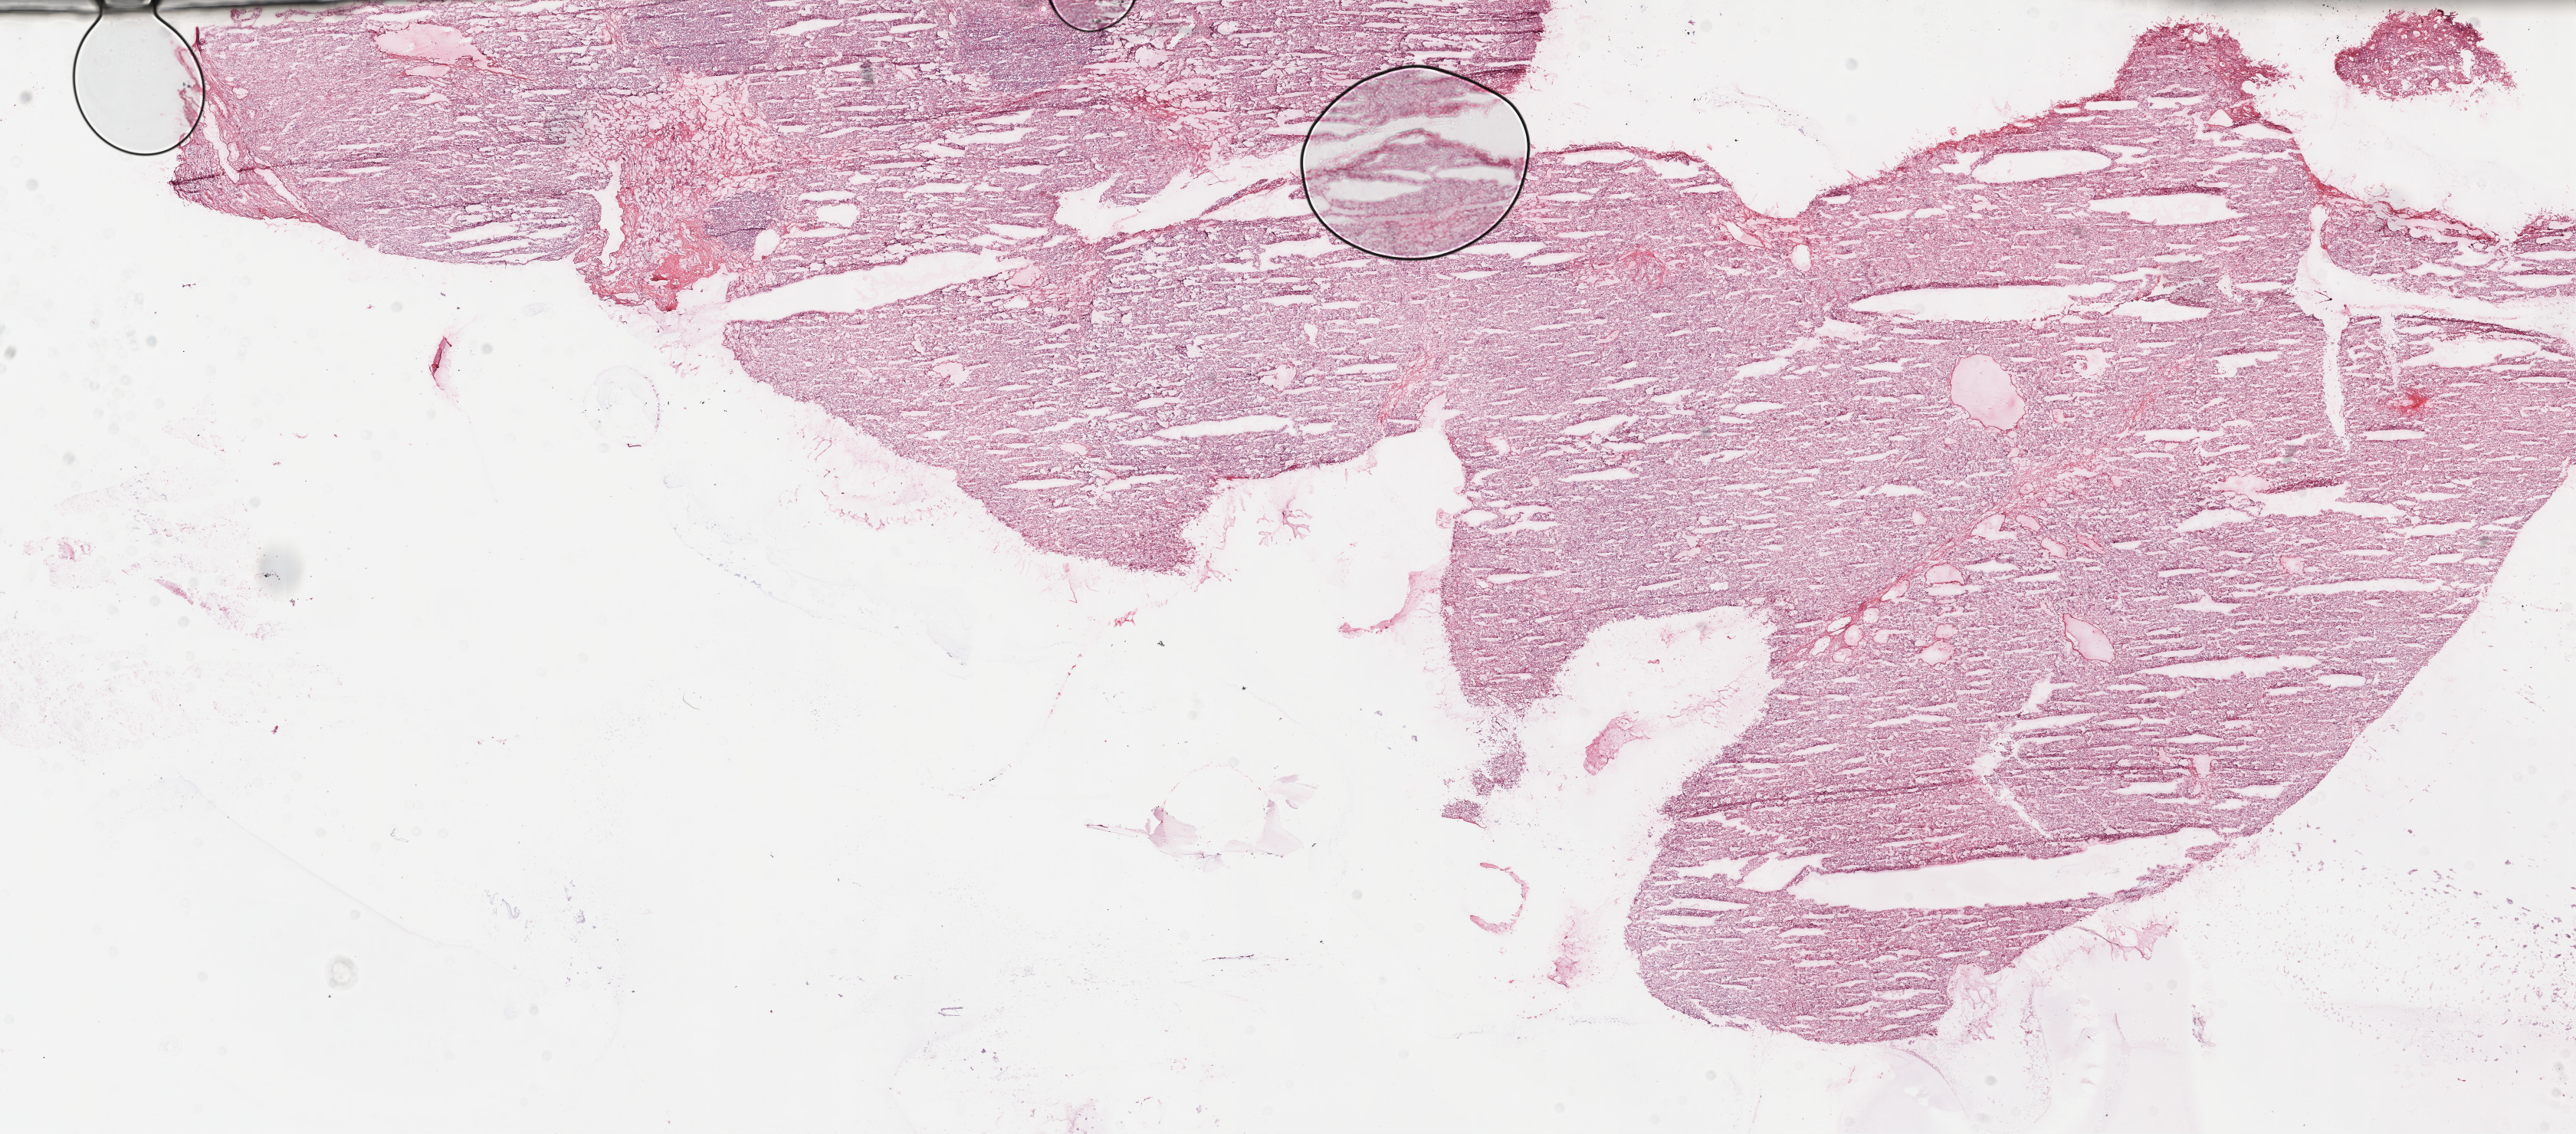
Whole-slide histology image, H&E-stained, low-resolution overview of the scanned area, about 27.2 x 12.0 mm. Frozen section from the top of the tissue portion. Kidney, primary tumour sample. Male, age 61 years at initial diagnosis. Histologic grade: G4 (undifferentiated). Pathologist review of this section (percent, as recorded): tumour cells 95%, tumour nuclei 90%, normal cells 0%, stromal cells 5%, necrosis 0%.
• pathologic diagnosis: Clear cell adenocarcinoma, NOS
• AJCC pathologic stage: III
• laterality: left